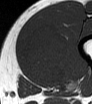
MRI of an extremity soft-tissue mass, one axial slice; position 20 of 62 along the scan axis; MR volume resampled by the dataset authors to the PET/CT grid (not the native acquisition matrix); 3.27 mm slice thickness; 92 × 104 image matrix, field of view 90 × 102 mm. Male patient. From the clinical record (not read from this slice): histological type: mixoid liposarcoma; grade: low; site of the primary tumour: left thigh.
Annotated regions visible in this slice (expert contour drawn on MRI and transferred to this co-registered scan by the dataset authors):
- gross tumour volume (mass): bounding box (x1, y1, x2, y2) in pixels: (23, 22, 68, 84)